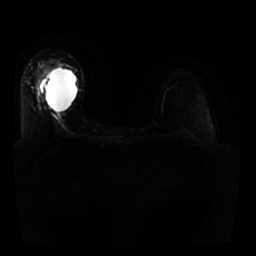
Breast MRI, one axial slice; position 17 of 25 along the scan axis; diffusion-weighted series; image 2 of 4 stored at this slice position (different b-values; order by instance number); 1.5 T; 256 × 256 image matrix, field of view 330 × 330 mm. Female patient.
Outlined on this slice (expert manual segmentation):
- tumour on diffusion-weighted imaging: bounding box [x1, y1, x2, y2] px = [40, 67, 60, 85]